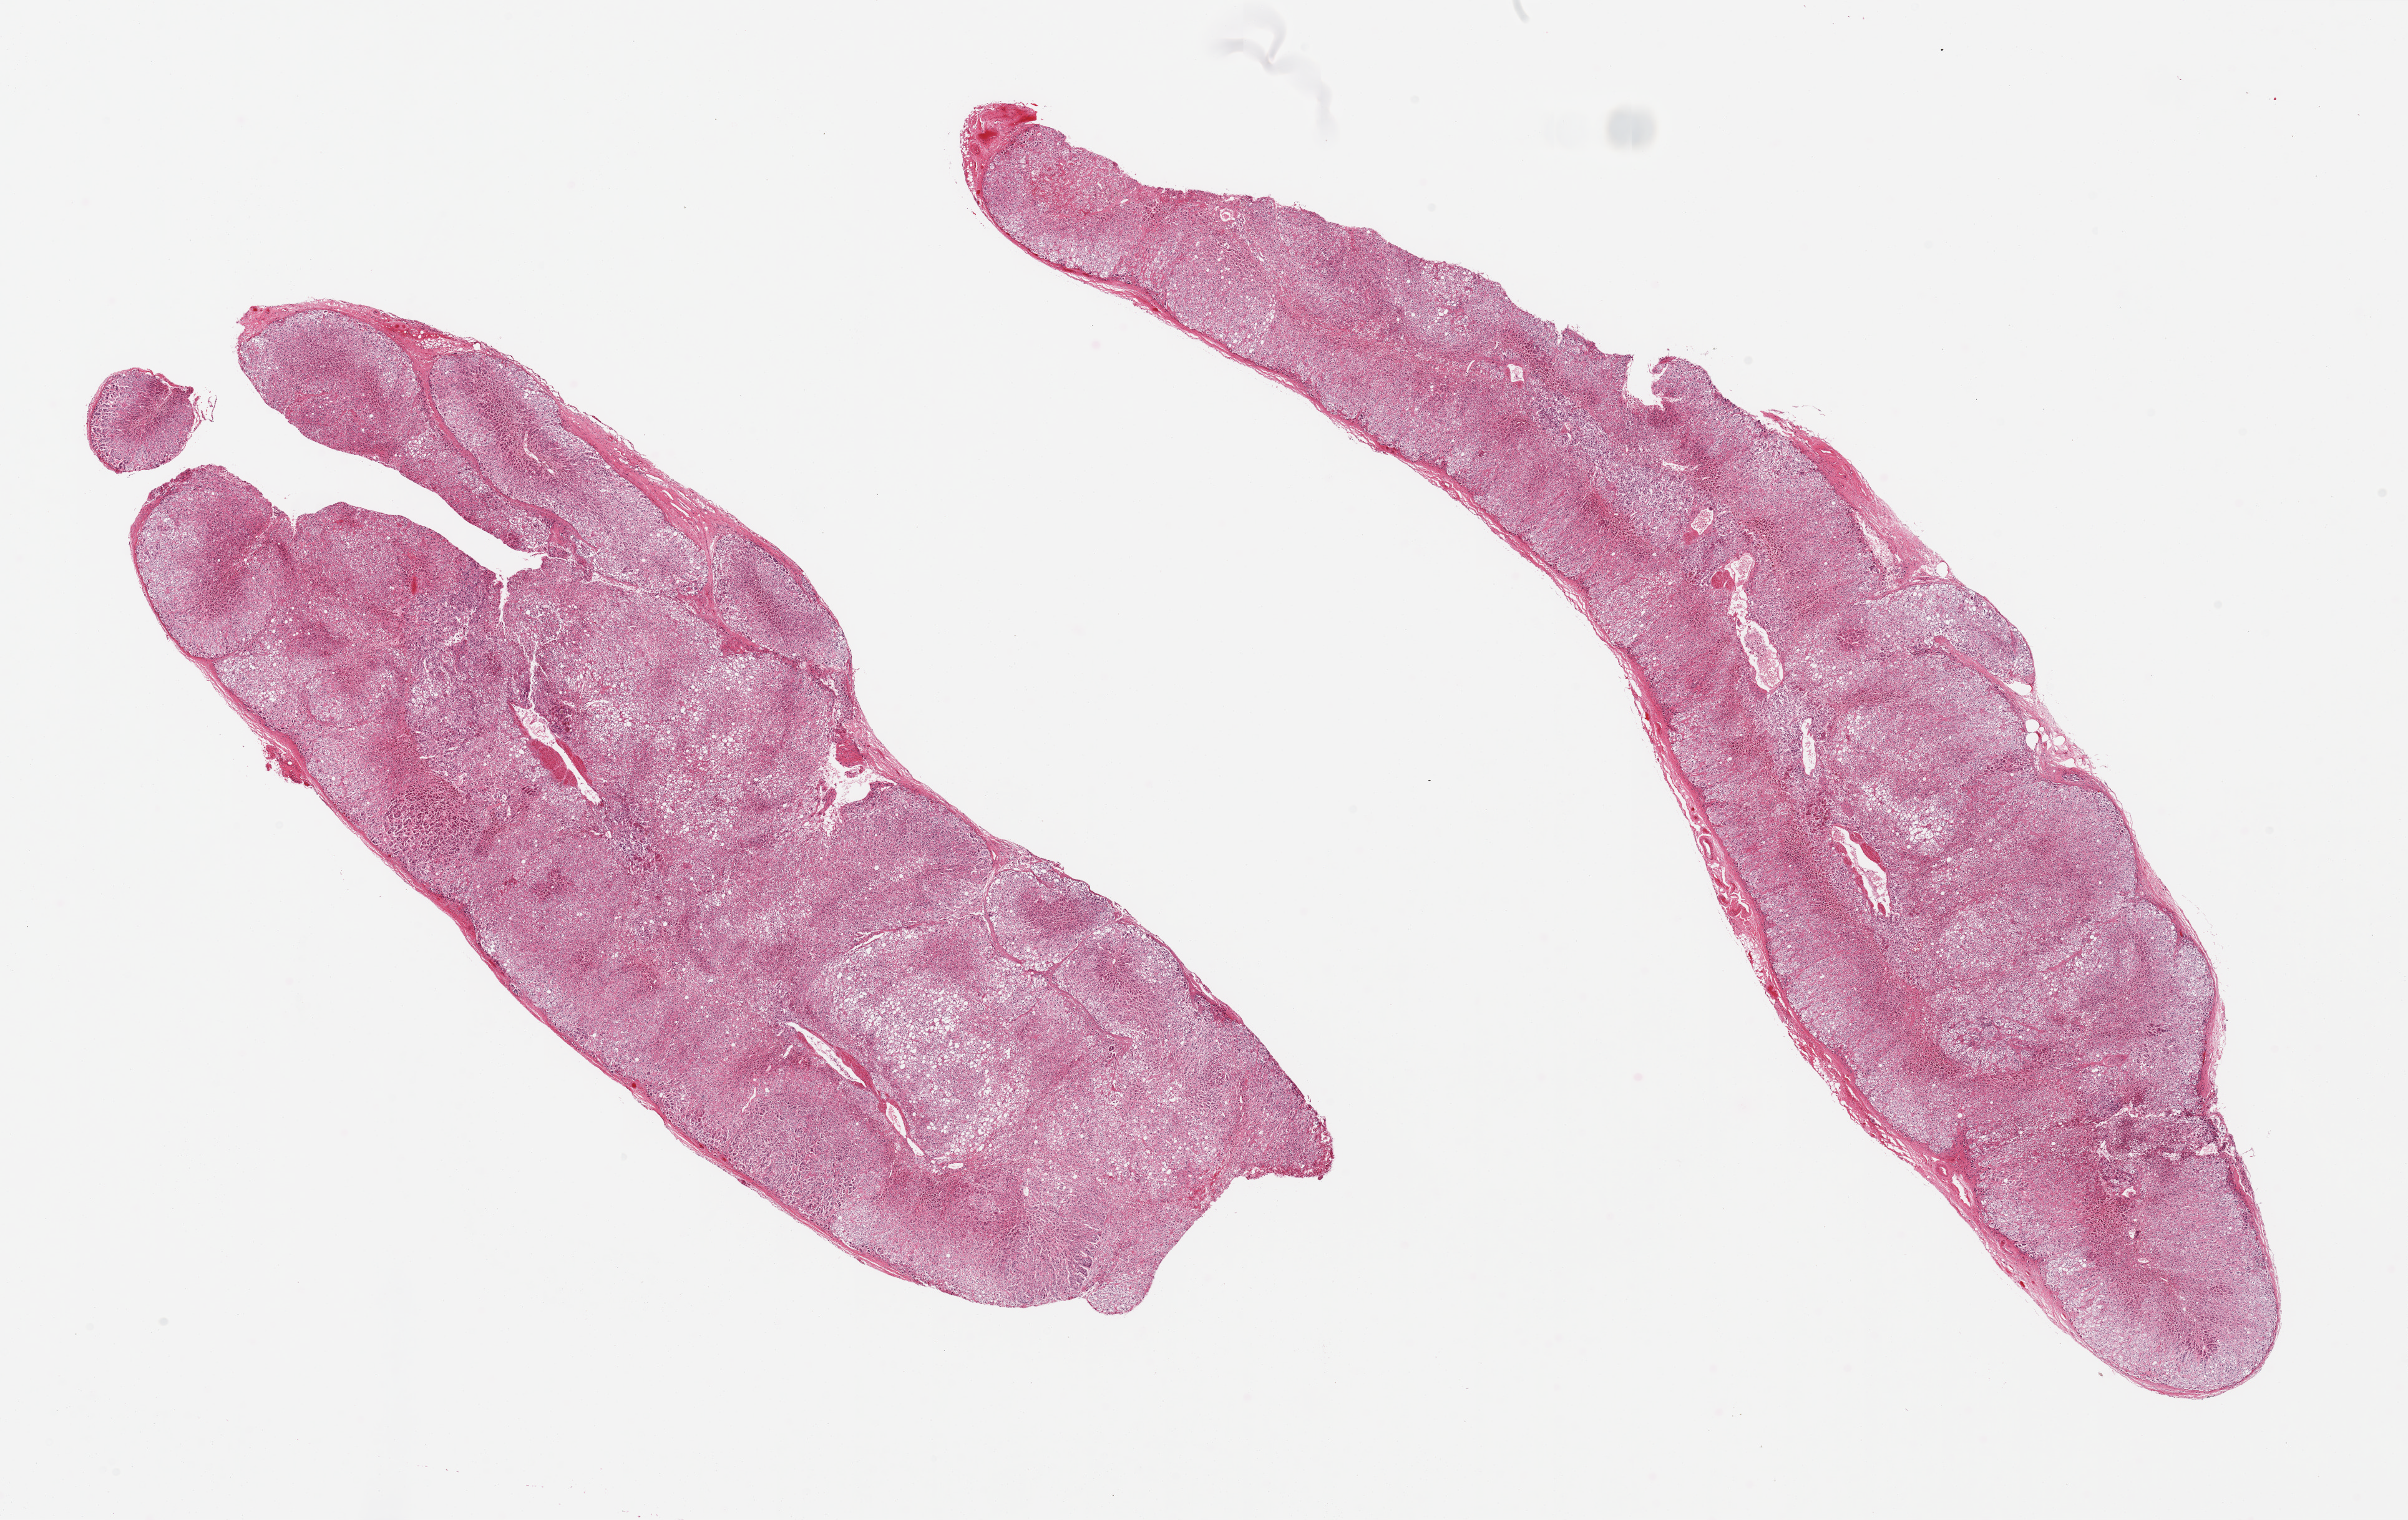
H&E whole-slide image, whole scanned area (about 30.5 x 19.3 mm, slide scanned at 20x) shown as a low-resolution overview; PAXgene-fixed, paraffin-embedded tissue; sampled site (target tissue): adrenal gland; tissue donor sample. Donor sex: female.
Reviewer comment on this tissue sample: 2 pieces; well trimmed.